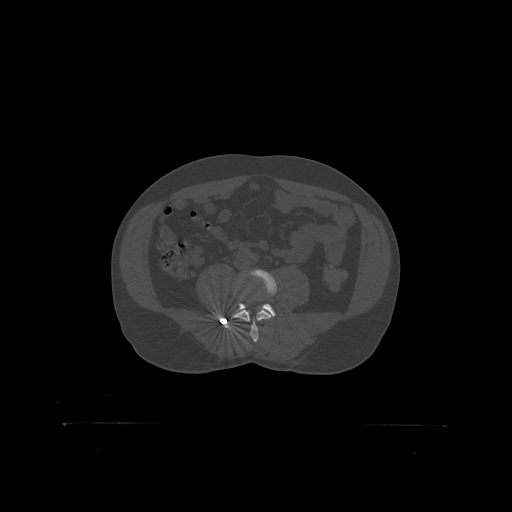
CT including the spine, one axial slice. Slice 223 of 399 in the series (ordered by position). 120 kVp. Bone window (W 1800 / L 400 HU). 1.25 mm slice thickness. 512 × 512 image matrix, field of view 650 × 650 mm. Patient: male, 46 years. Case-level facts recorded for this patient, not image findings: primary cancer: skin.
Outlined on this slice (semi-automatically segmented with operator editing):
- L4 vertebra: bounding box [x1, y1, x2, y2] px = [235, 270, 277, 319]
- L5 vertebra: [237, 303, 276, 316]